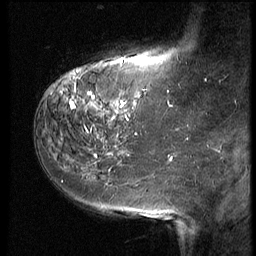
Breast MRI (dynamic contrast-enhanced), one sagittal slice. Slice 17 of 64 in the series (ordered by position). 3 images stored at this slice position (order not interpretable as contrast timing). 1.5 T. TE 4.2 ms, TR 9 ms. 2.5 mm slice thickness. 256 × 256 image matrix, field of view 180 × 180 mm. Patient: female, 59 years. Case-level facts recorded for this patient, not image findings: setting: breast cancer imaged before/during neoadjuvant chemotherapy; receptor status: HER2-positive.
Outlined on this slice (semi-automatic segmentation, software-assisted and operator-edited):
- analysis volume of interest (the breast-tissue region the enhancement analysis was run in; not a lesion): bounding box (x1, y1, x2, y2) in pixels: (54, 65, 155, 132)
- tumour enhancement mask (voxels above the 140 % enhancement threshold inside the analysis volume of interest): (61, 73, 136, 118)